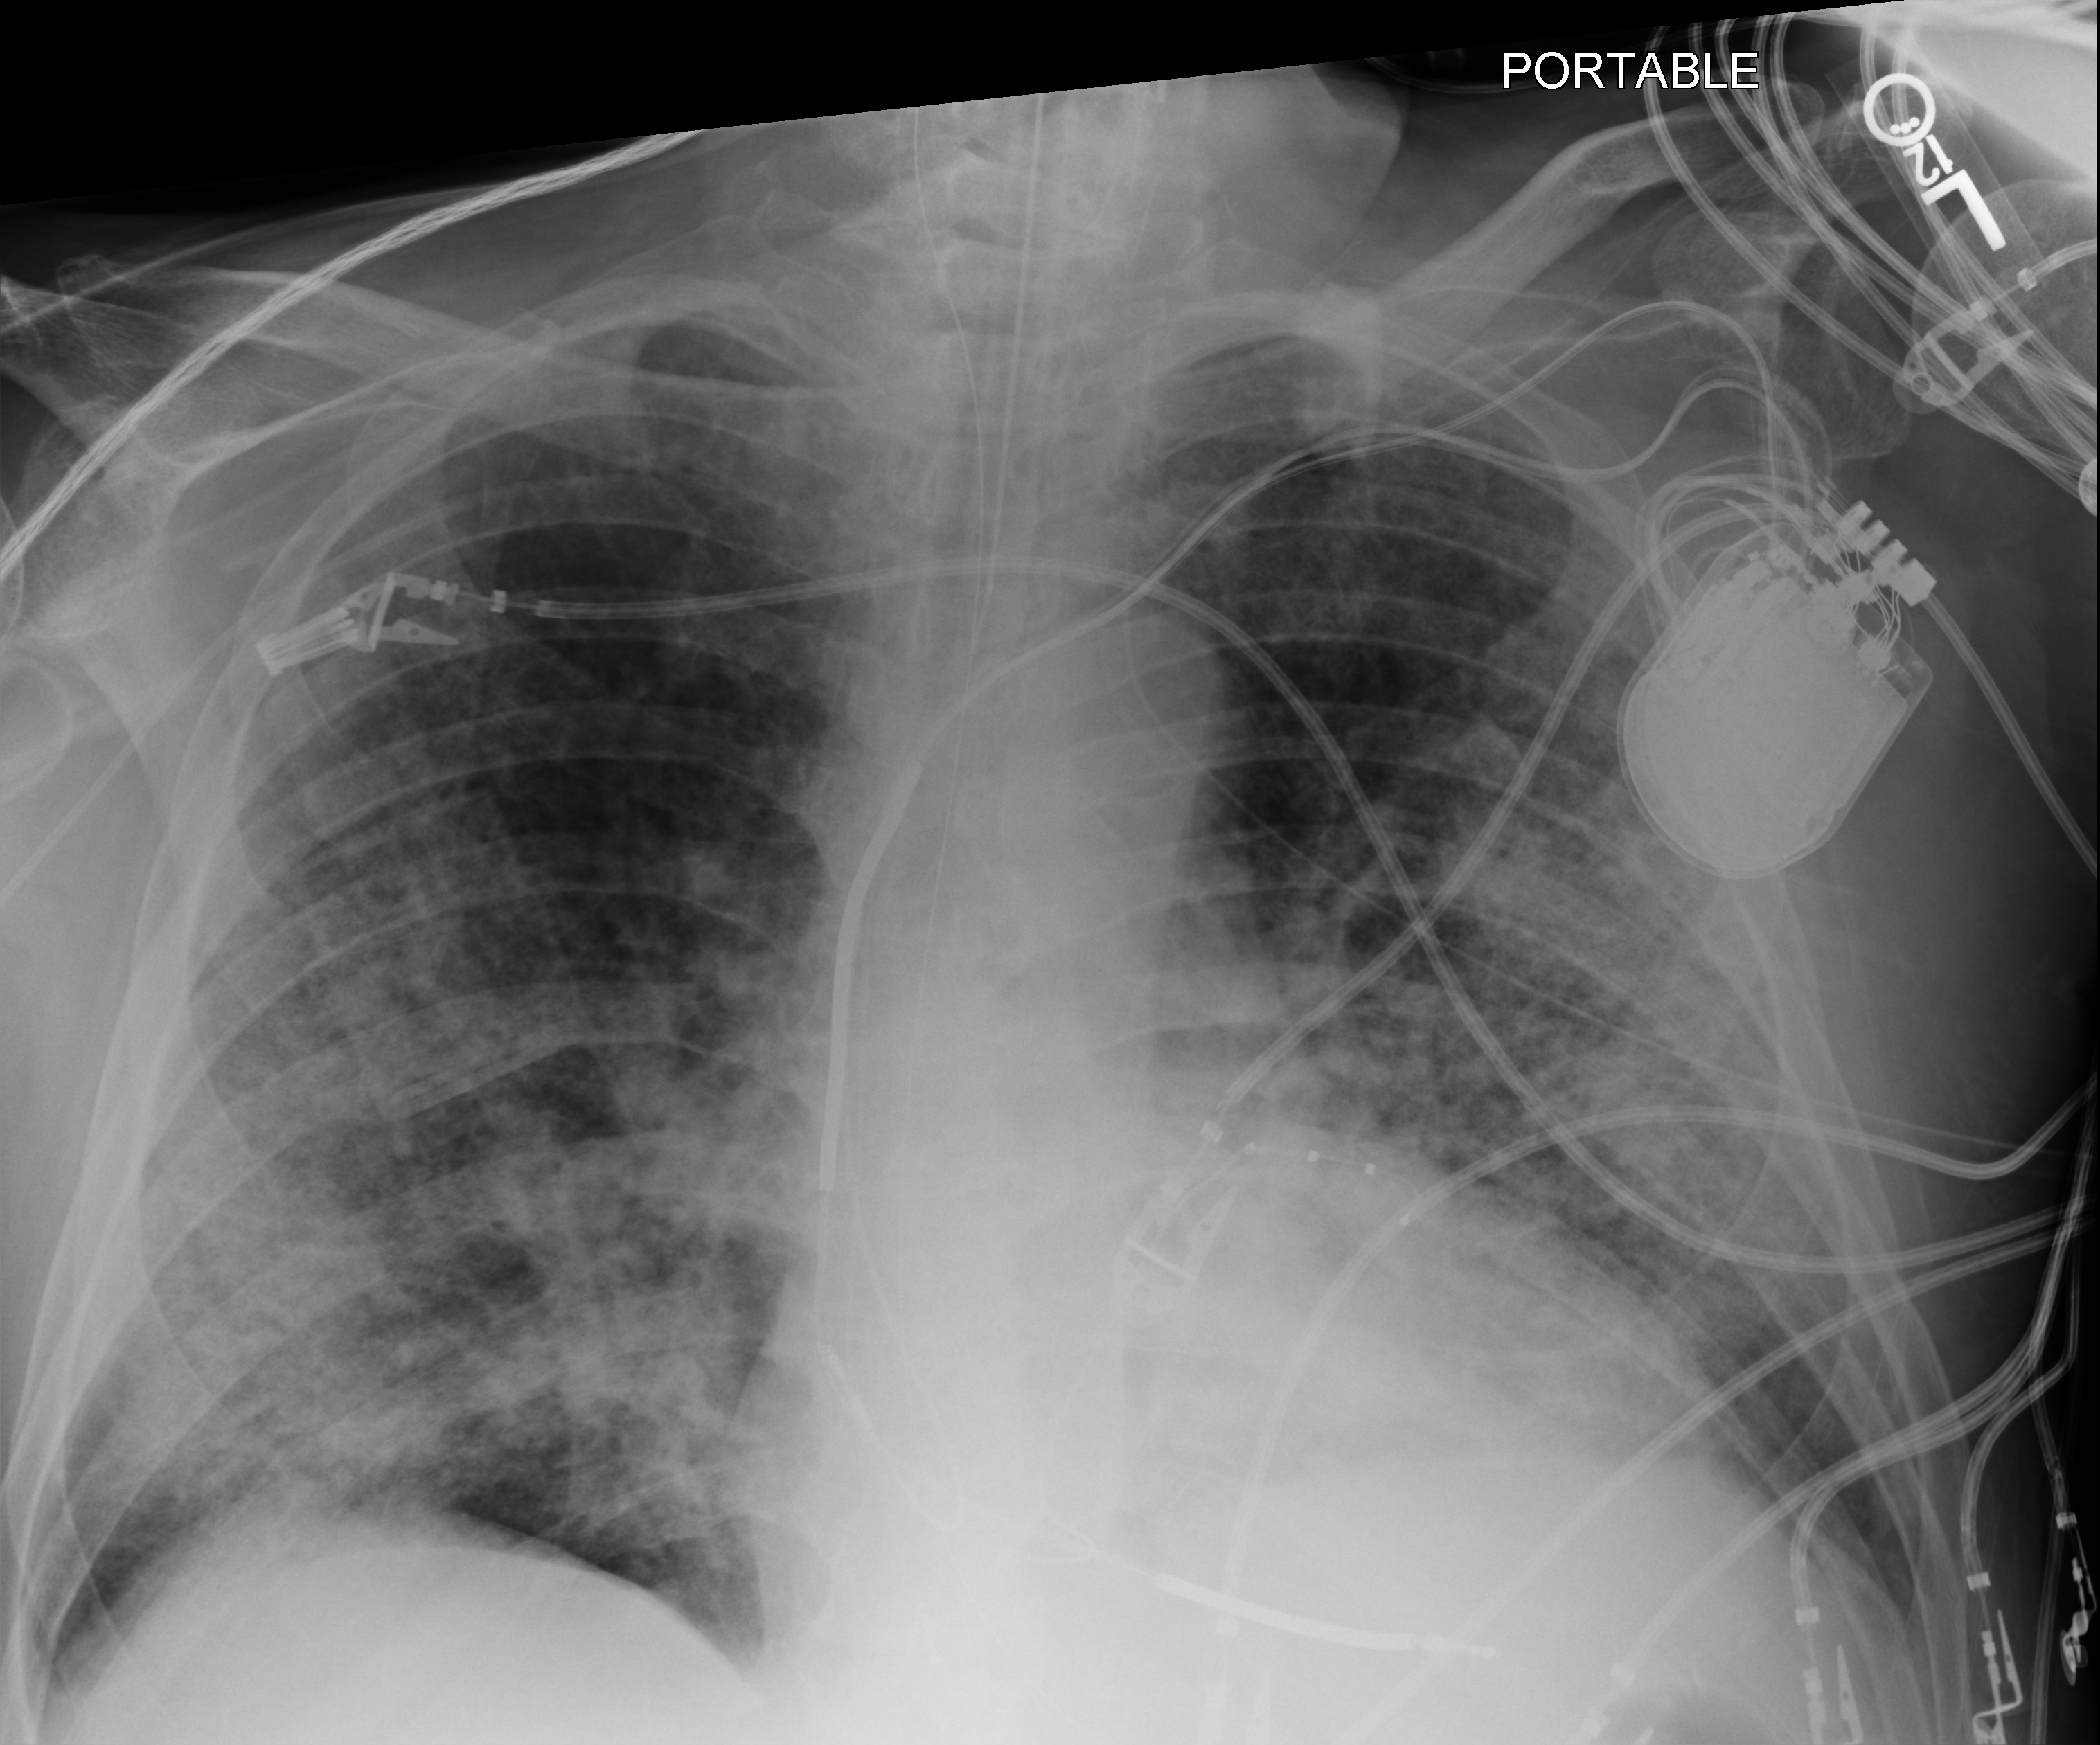
Chest X-ray (portable). Patient hospitalised with COVID-19; male, aged 60–74 years.
Hospital-stay facts (about this admission, not read from this image; timing relative to this image not recorded): admitted to intensive care during this hospital stay: yes; mechanically ventilated during this hospital stay: yes; other chronic lung disease (admission record): no.